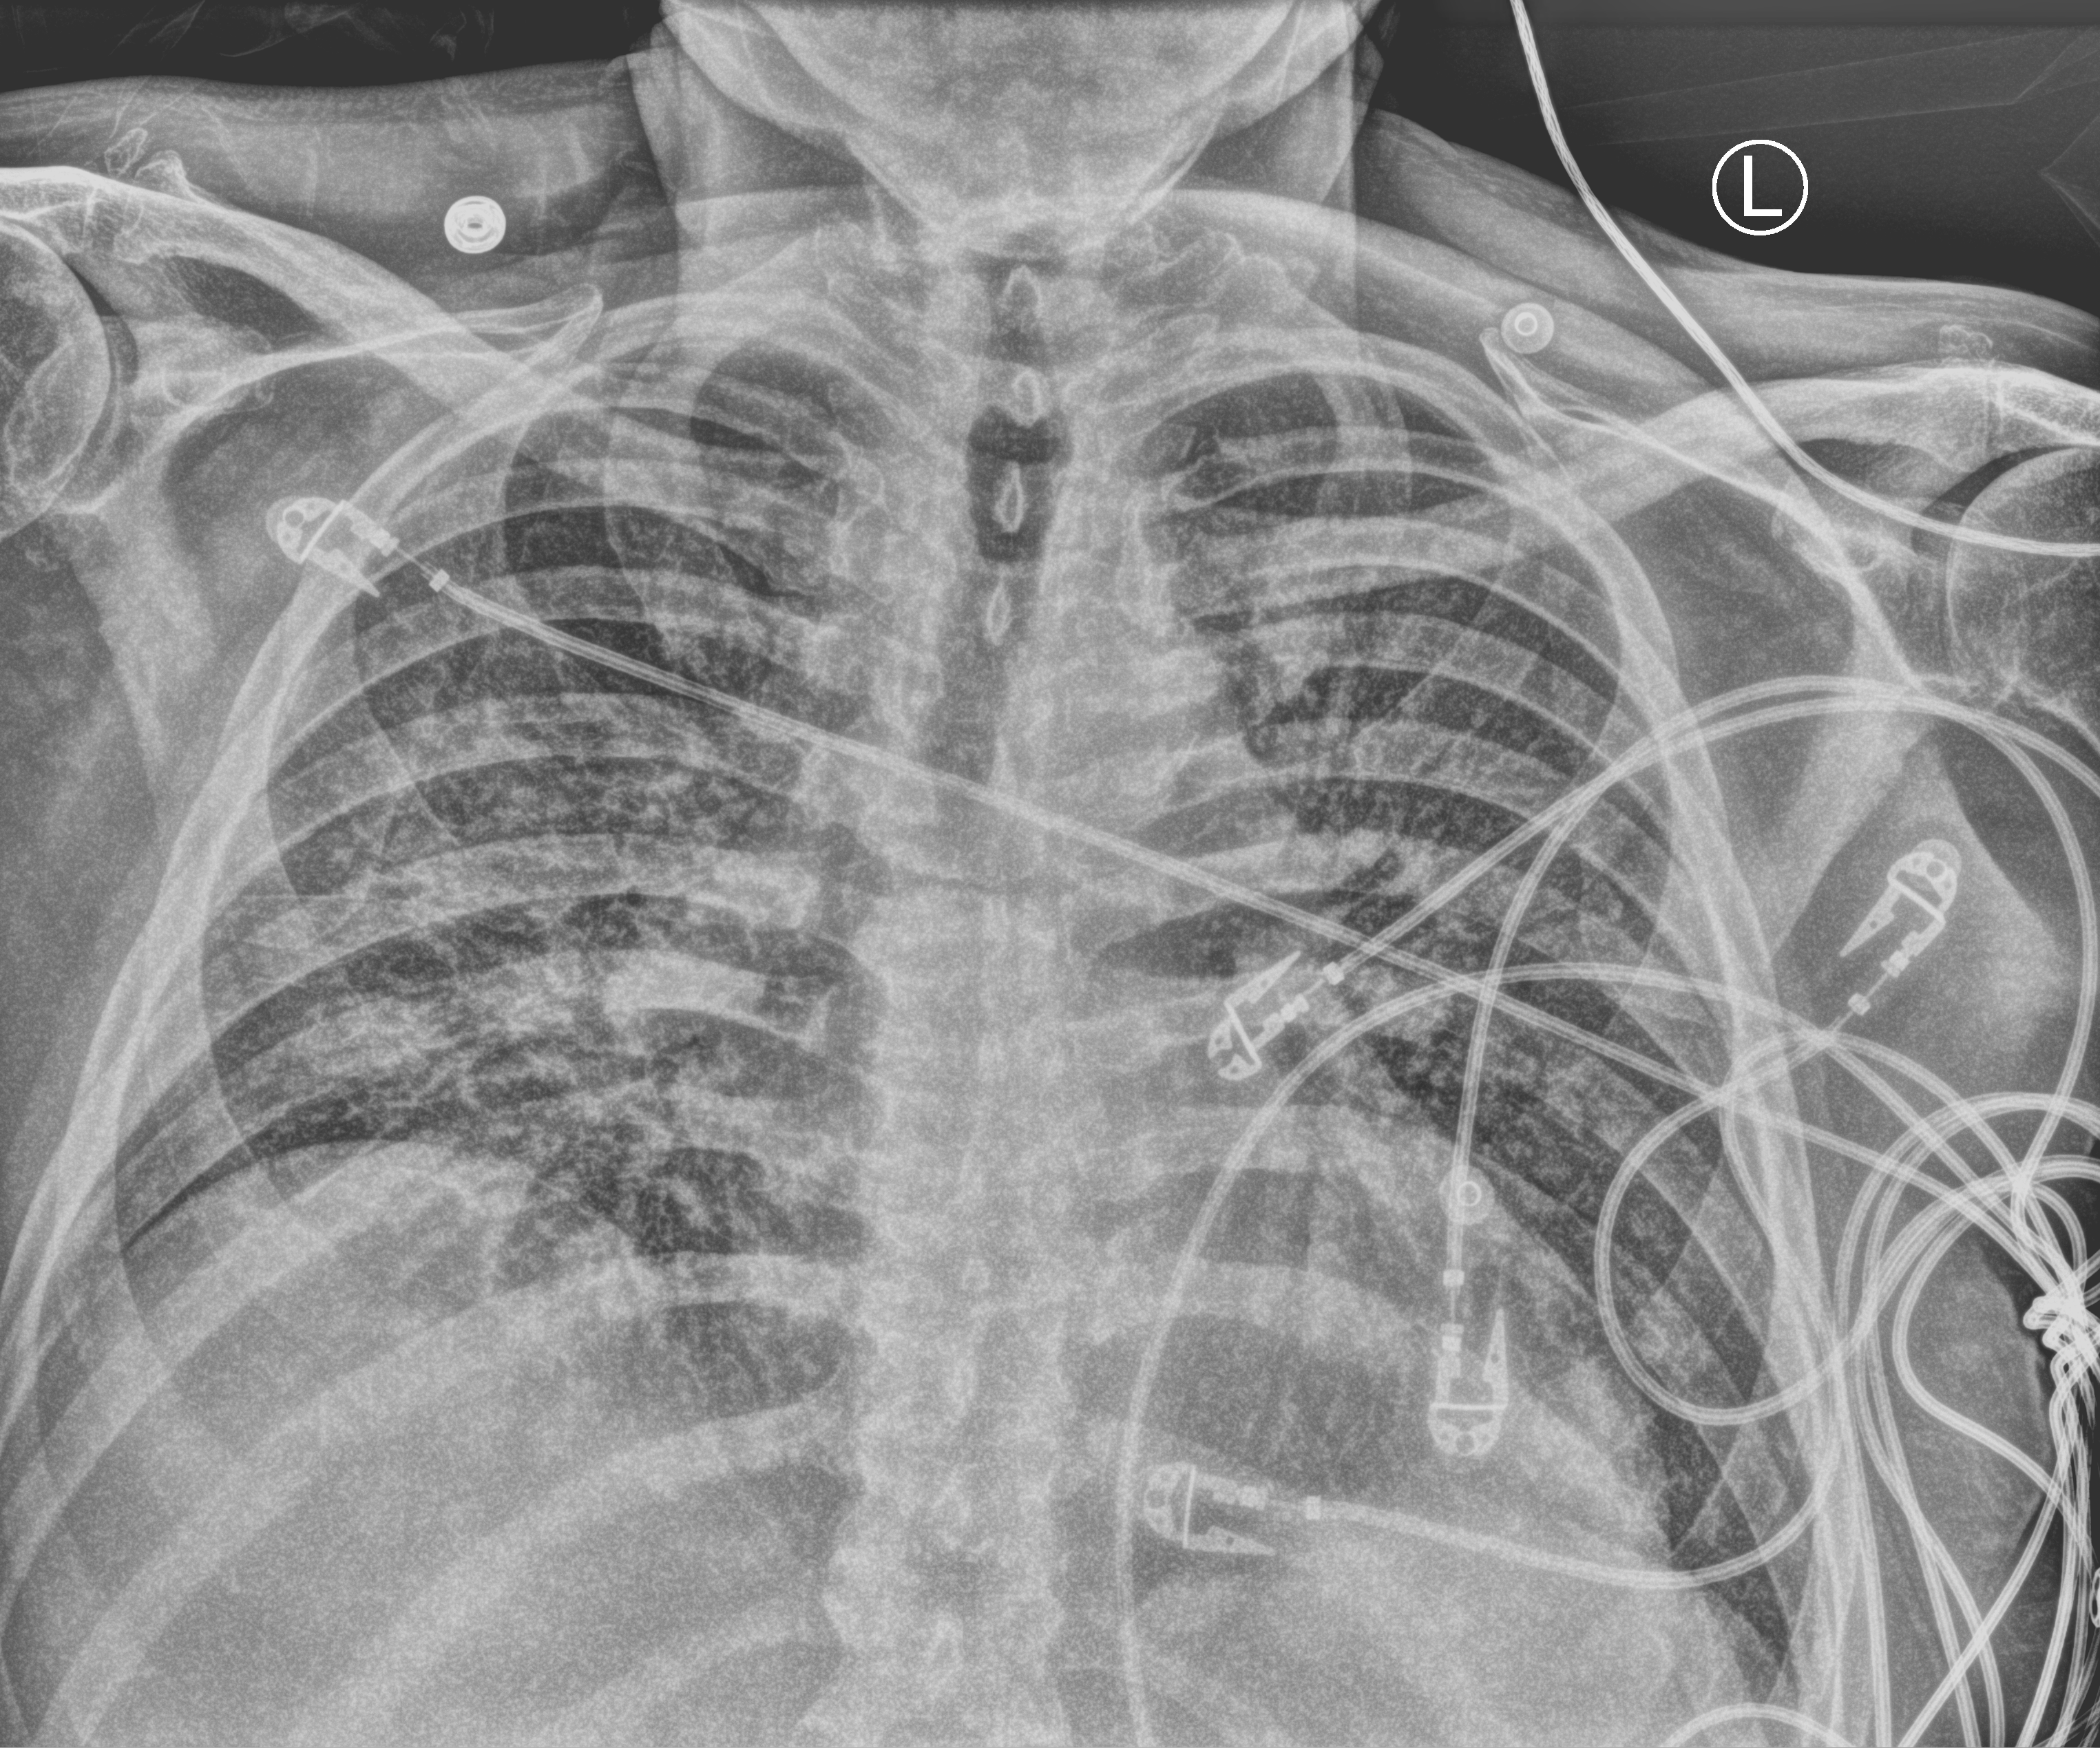
Bedside chest radiograph (computed radiography), anteroposterior (AP) projection. Patient hospitalised with COVID-19; male, aged 60–74 years.
Admission-level facts for this patient (not findings on this image; timing relative to this image not recorded): smoking status (admission record): former.